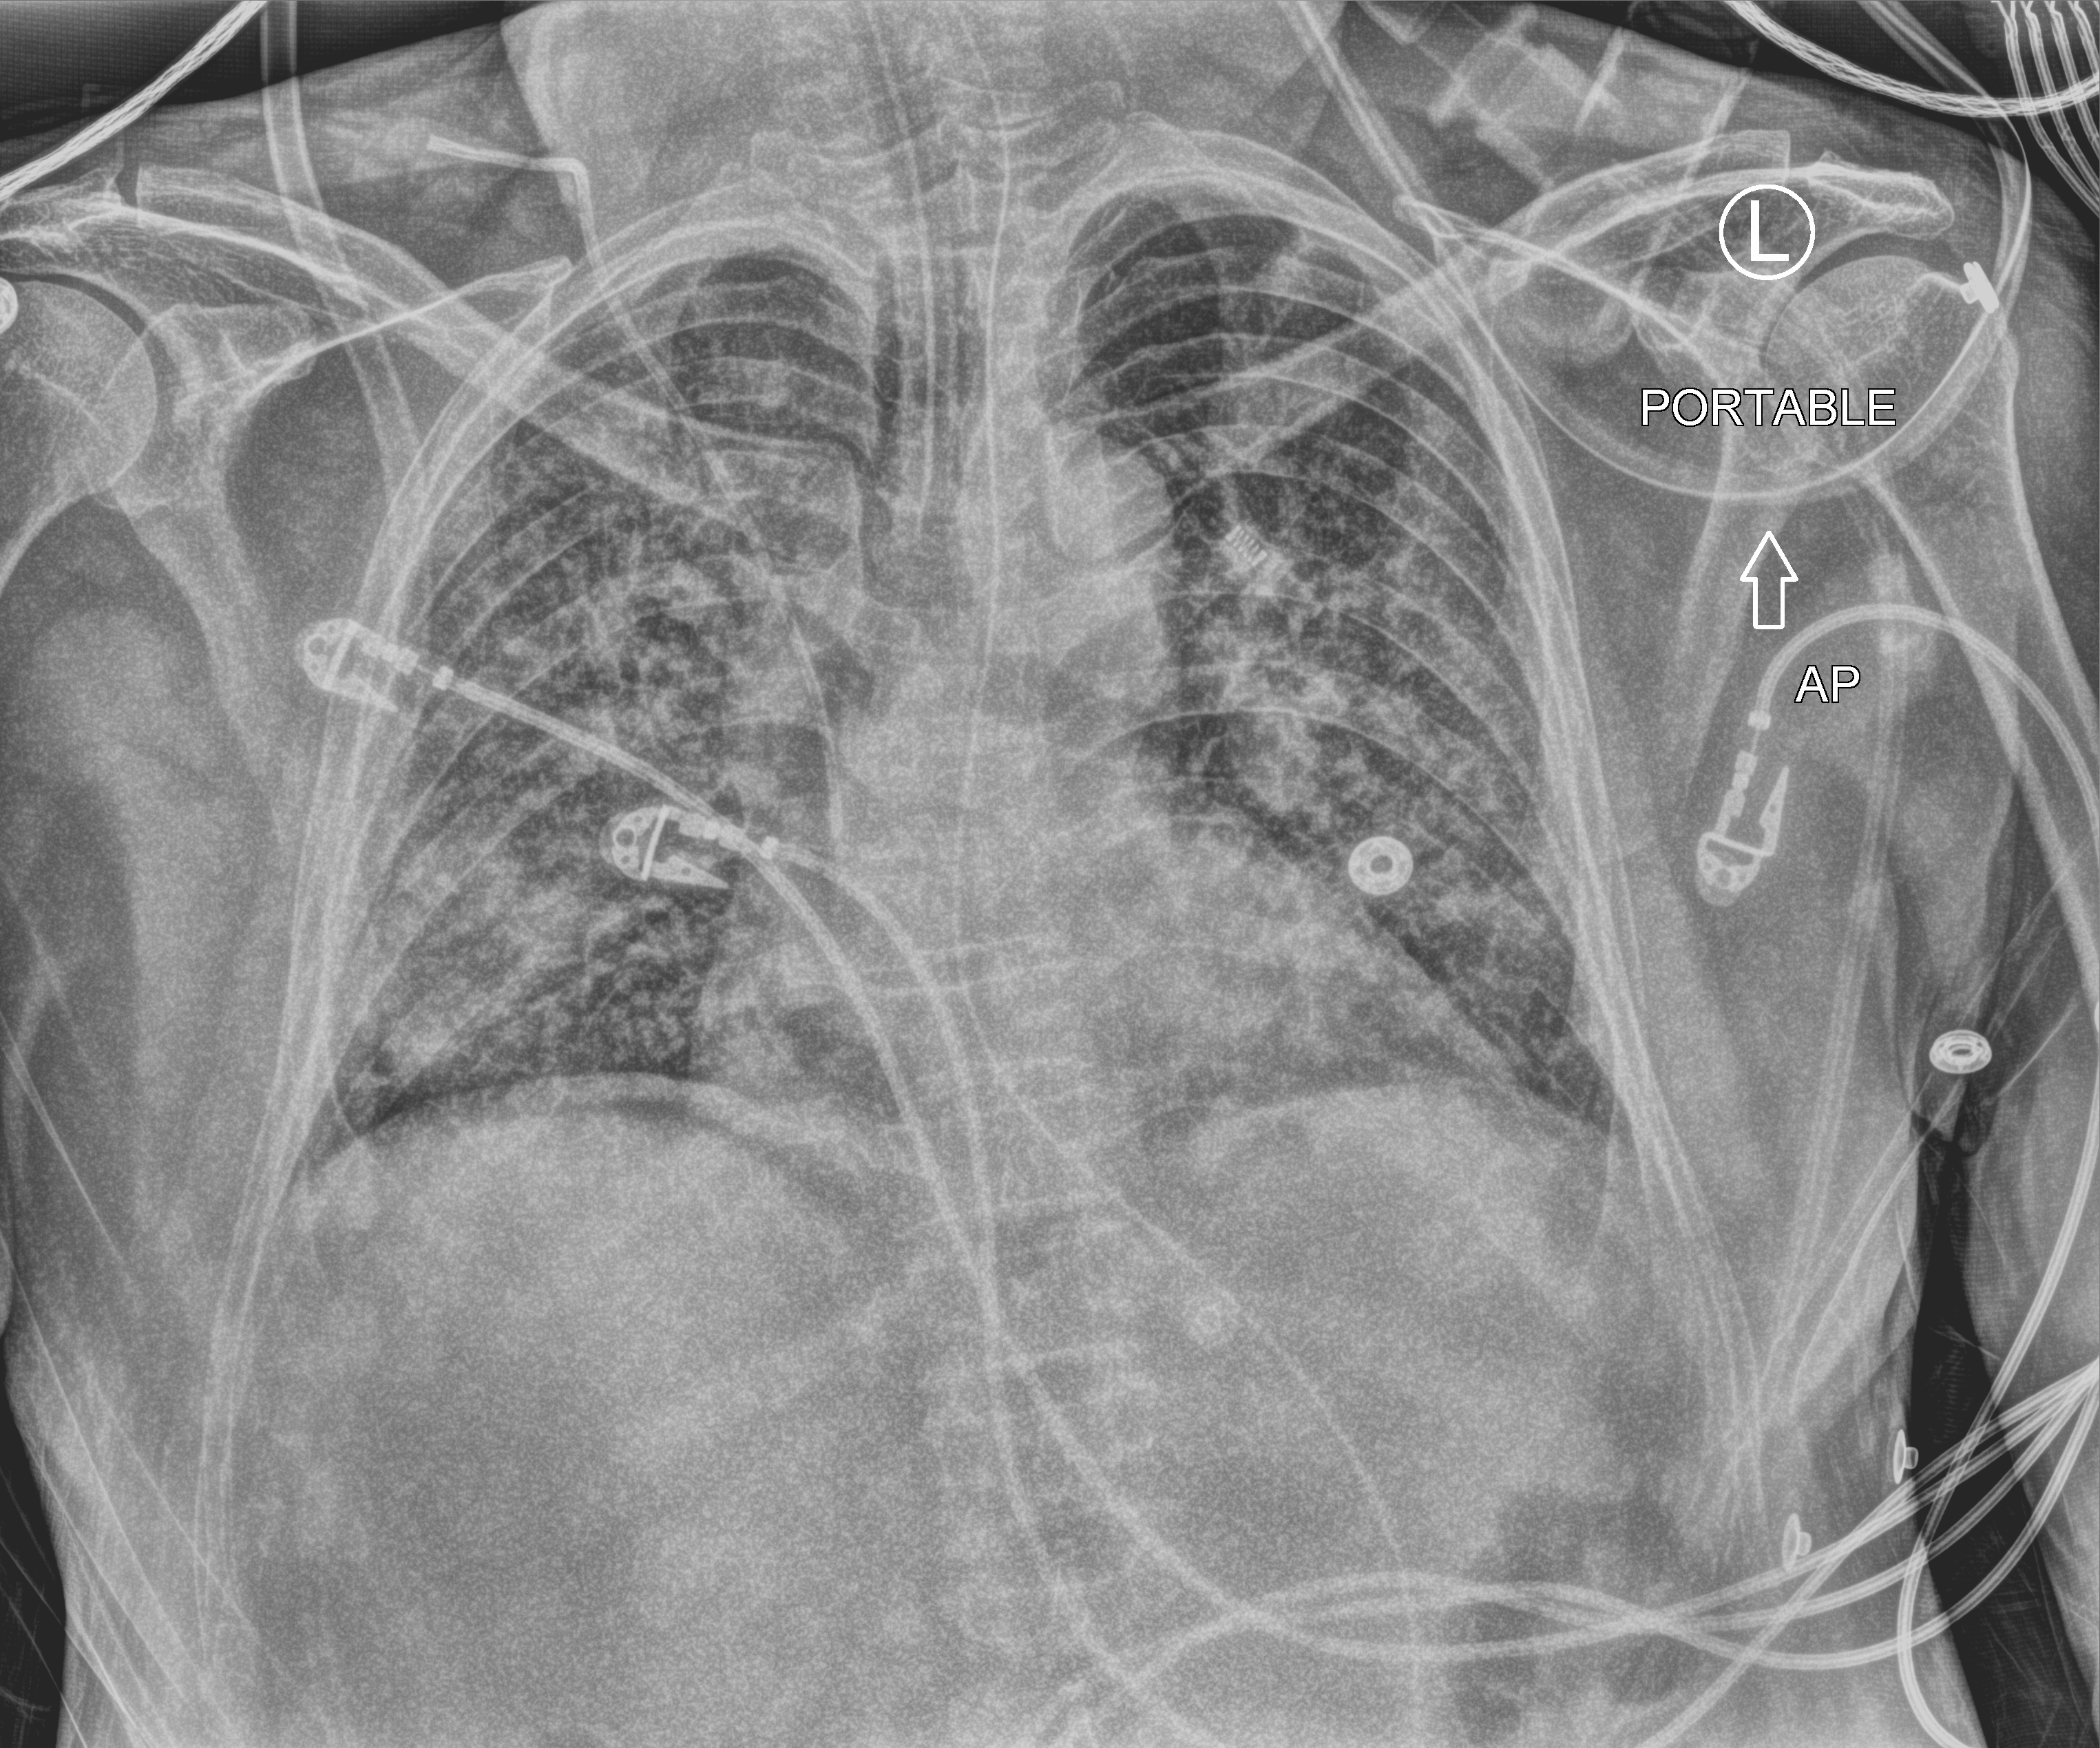
Portable chest radiograph, anteroposterior (AP) projection. Patient hospitalised with COVID-19; male, aged 60–74 years.
From the hospital-stay record, not from the radiograph (when in the stay this image was taken is not recorded): length of hospital stay: 19 days; admitted to intensive care during this hospital stay: yes.